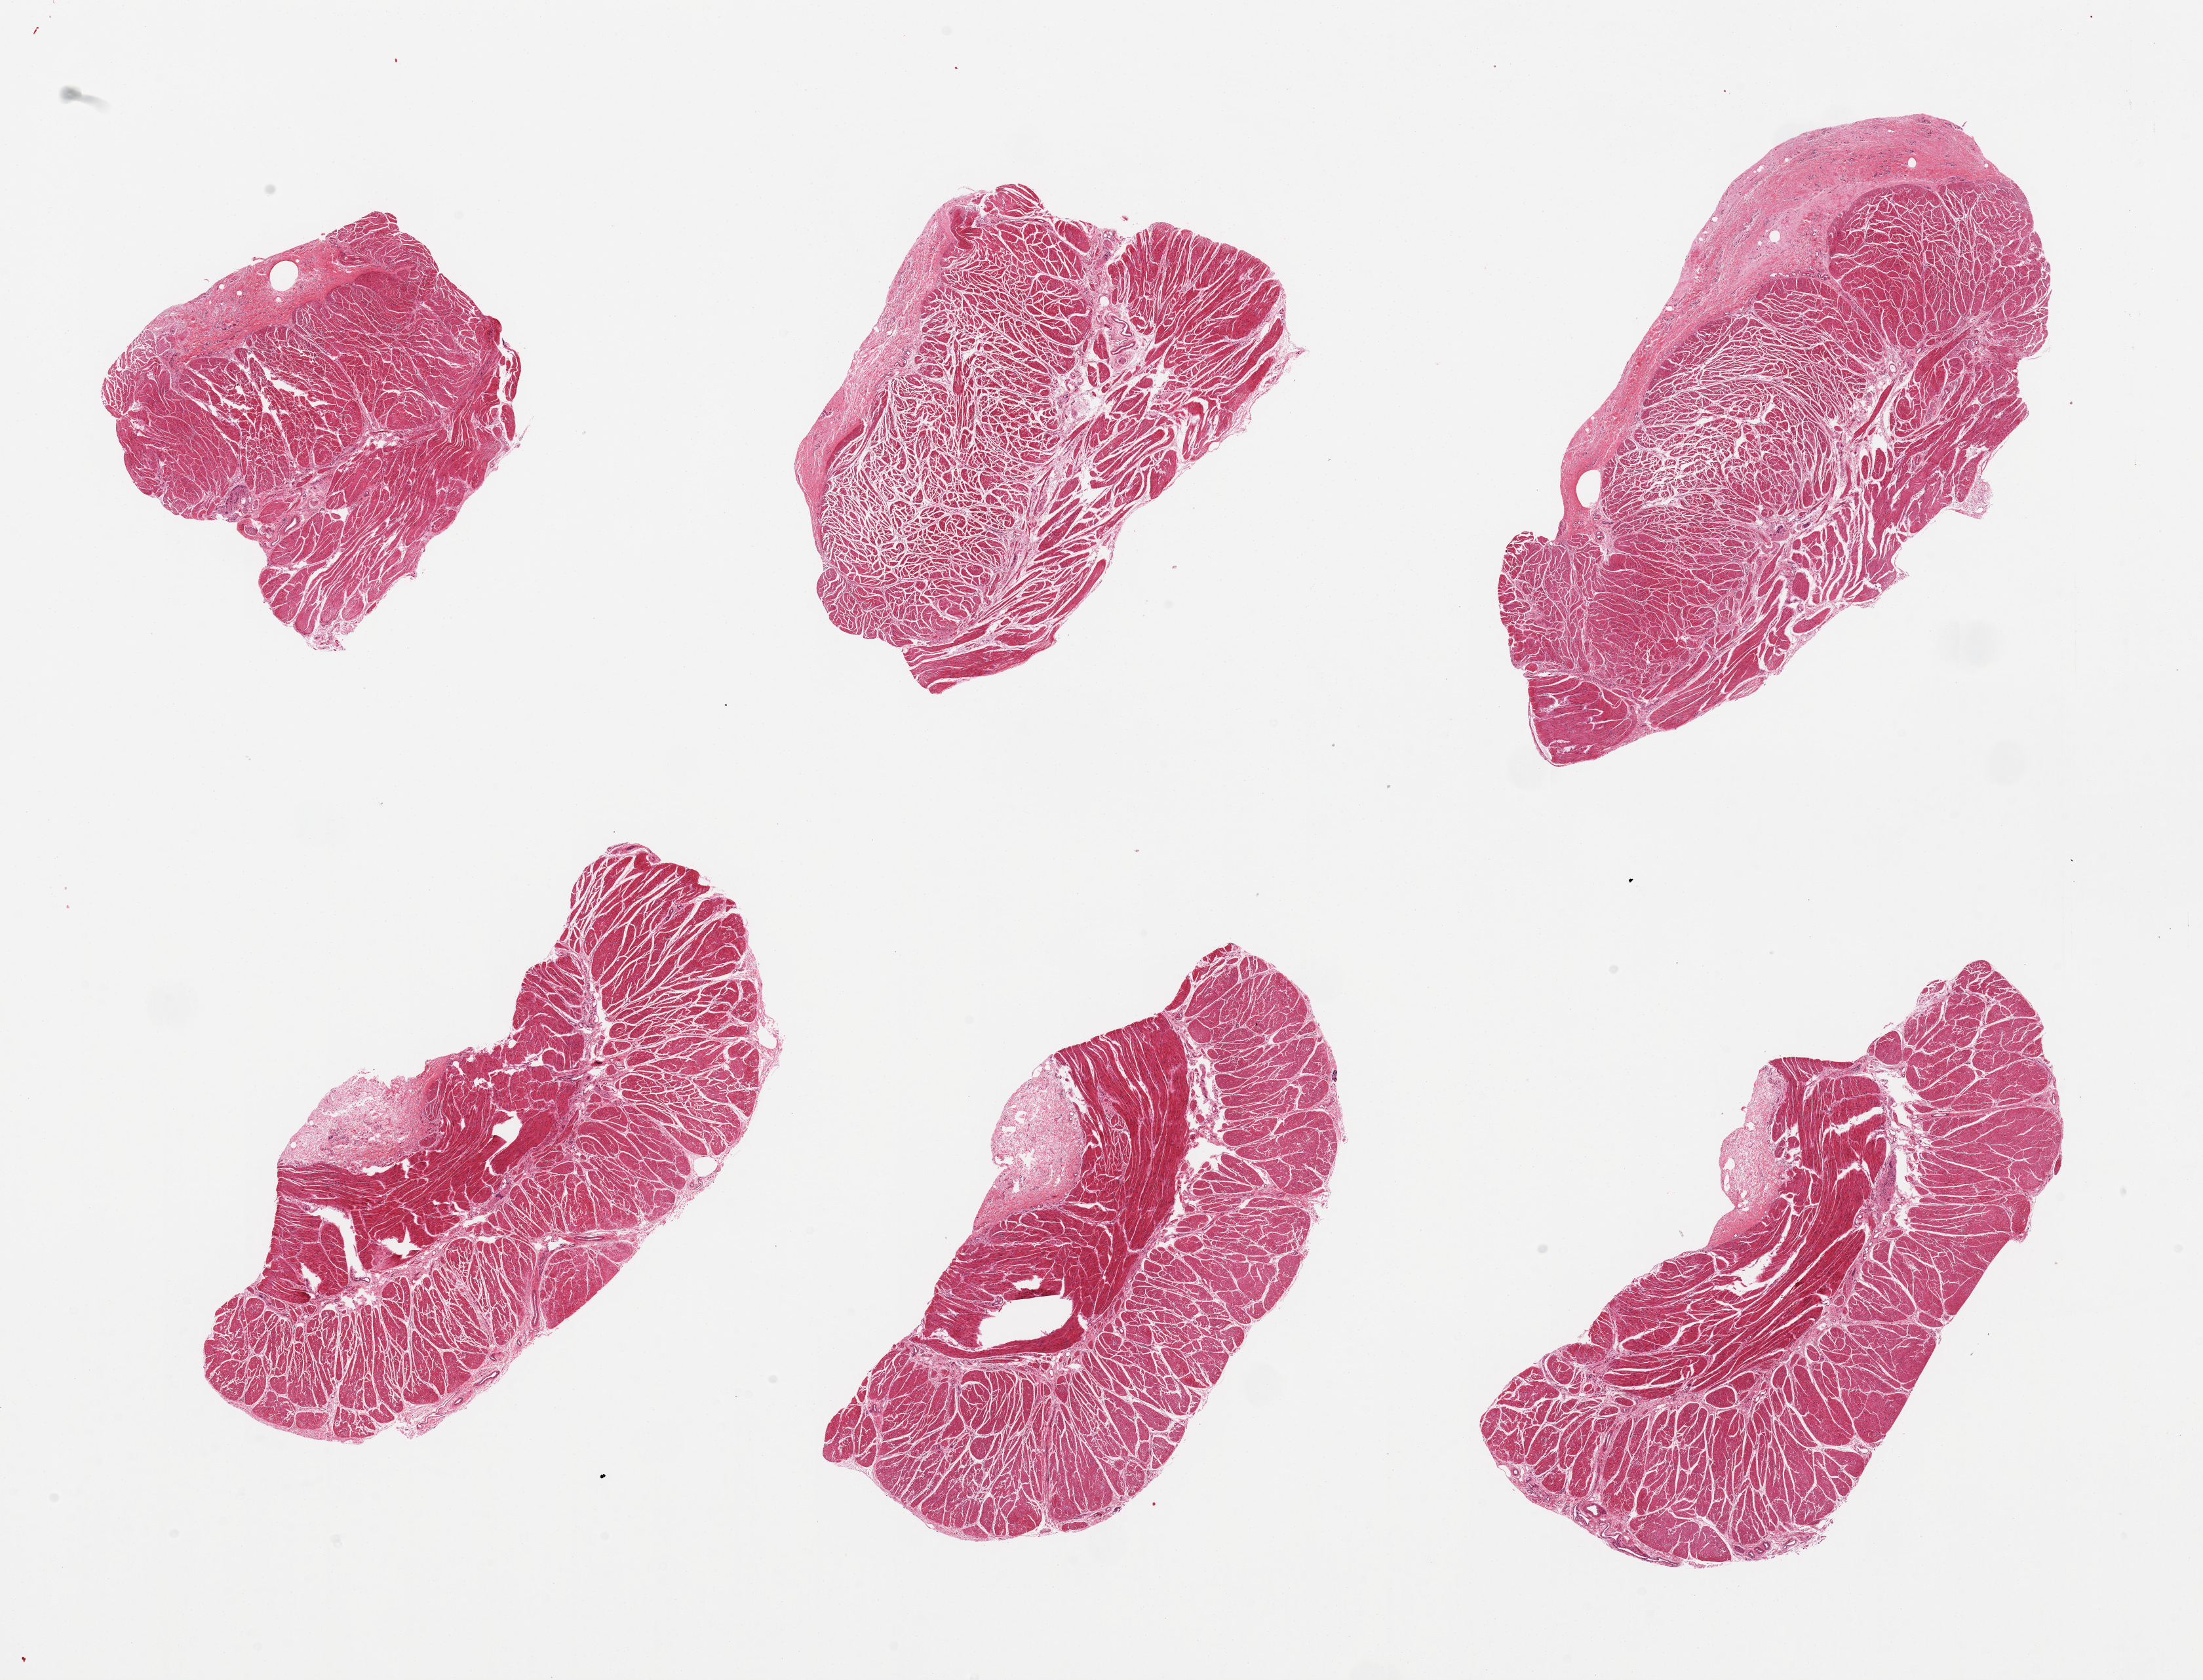
Digitized H&E-stained section — low-resolution overview of the scanned area, about 26.6 x 20.3 mm. PAXgene-fixed paraffin-embedded (PFPE) section. Target tissue: esophageal muscle. Tissue donor sample.
Review note (as recorded): 6 pieces, all muscularis.